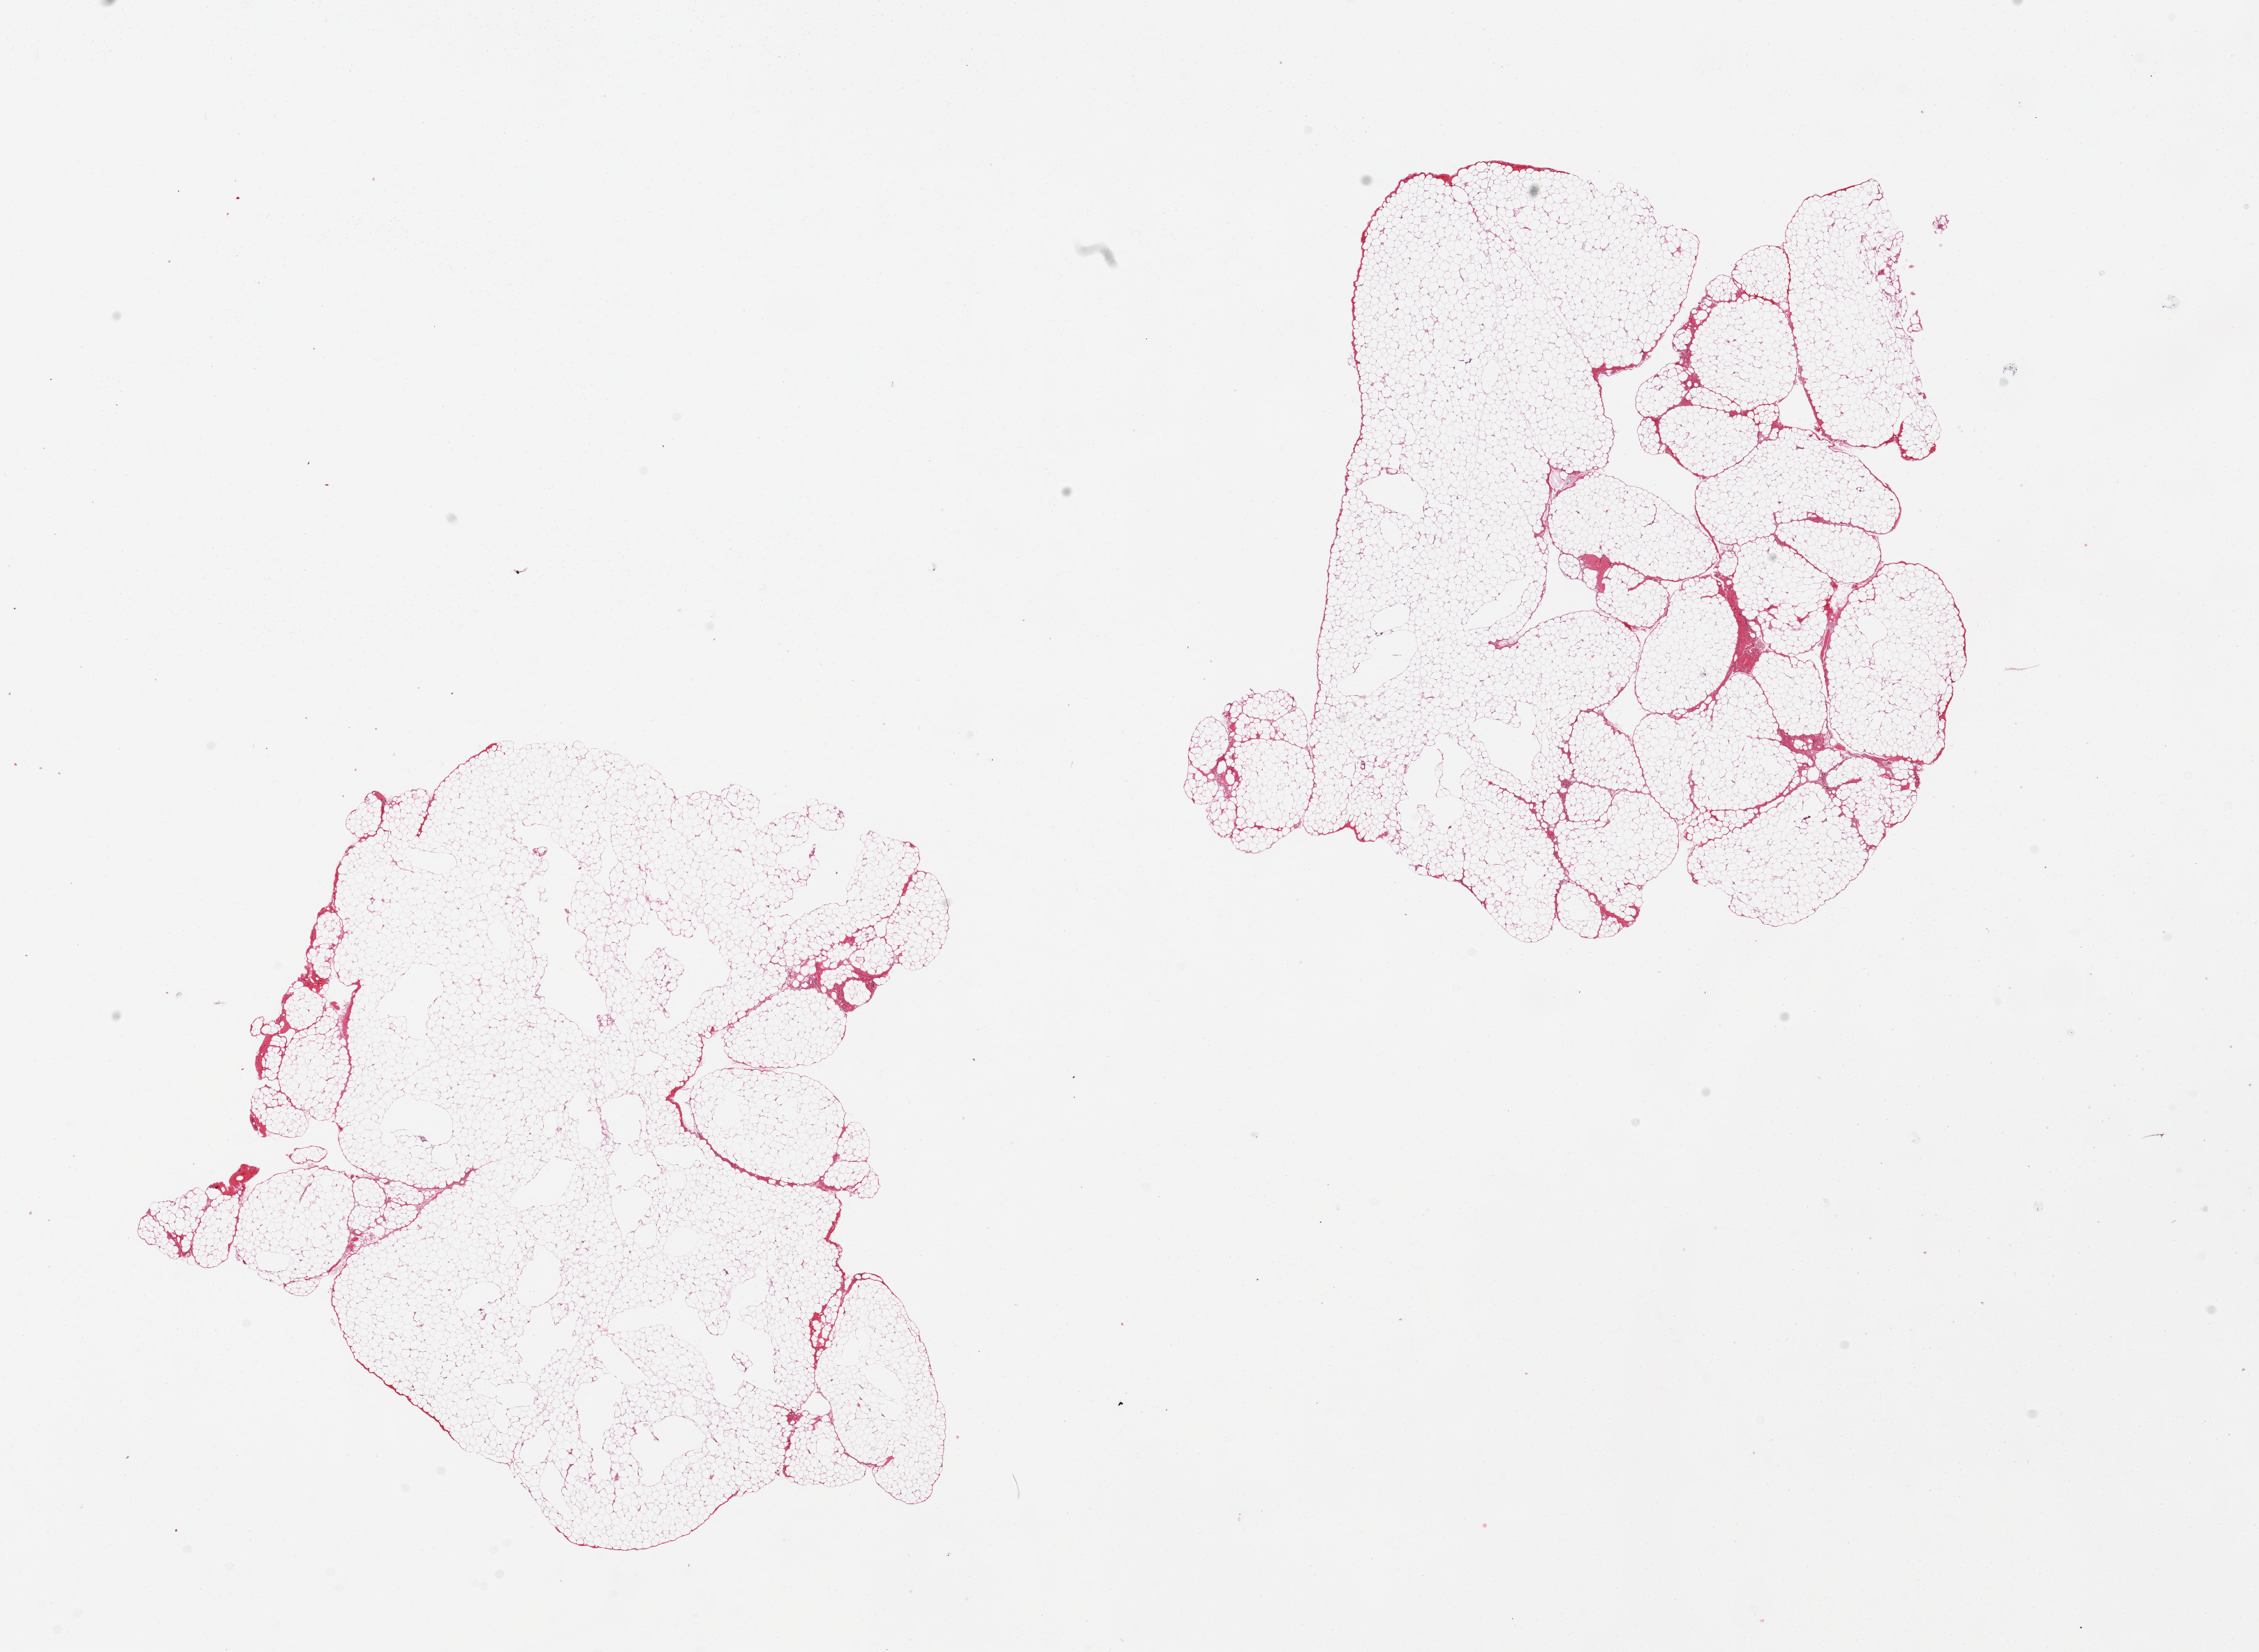
Whole-slide image, H&E stain — whole scanned area (about 25.6 x 18.7 mm) shown as a low-resolution overview. PAXgene-fixed paraffin-embedded (PFPE) section. Section of omentum (target tissue). Donor tissue sample. Male donor.
Pathologist's review note for this sample: 2 pieces, no abnormalities; minimal fibrosis.